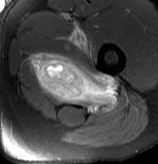
MRI of an extremity soft-tissue mass, one axial slice. Slice 61 of 70 in the series (ordered by position). T2-weighted fat-saturated. MR volume resampled by the dataset authors to the PET/CT grid (not the native acquisition matrix). 3.27 mm slice thickness. 158 × 164 image matrix, field of view 154 × 160 mm. Male patient. Case-level facts recorded for this patient, not image findings: histological type: extraskeletal osteosarcoma; grade: high; site of the primary tumour: left adductur.
Annotated regions visible in this slice (expert contour drawn on MRI and transferred to this co-registered scan by the dataset authors):
- gross tumour volume (mass): box from (x=31, y=23) to (x=119, y=115) px